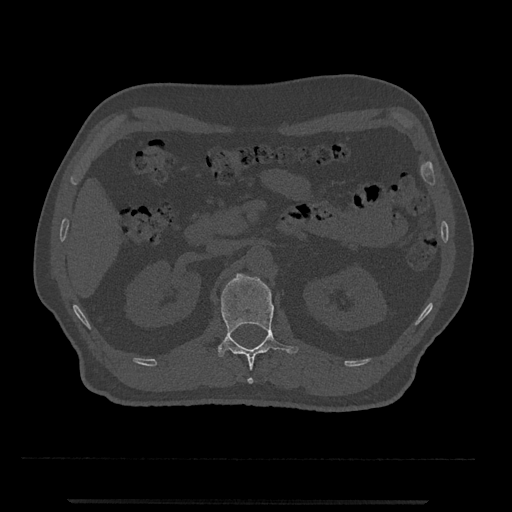
CT including the spine, one axial slice; slice 332 of 797 in the series (ordered by position); 120 kVp; bone window (W 1800 / L 400 HU); 0.5 mm slice thickness; 512 × 512 image matrix. Male patient, age 63 years. From the clinical record (not read from this slice): primary cancer: prostate.
Annotated regions visible in this slice (semi-automatically segmented with operator editing):
- L1 vertebra: bounding box (x1, y1, x2, y2) in pixels: (217, 274, 299, 384)